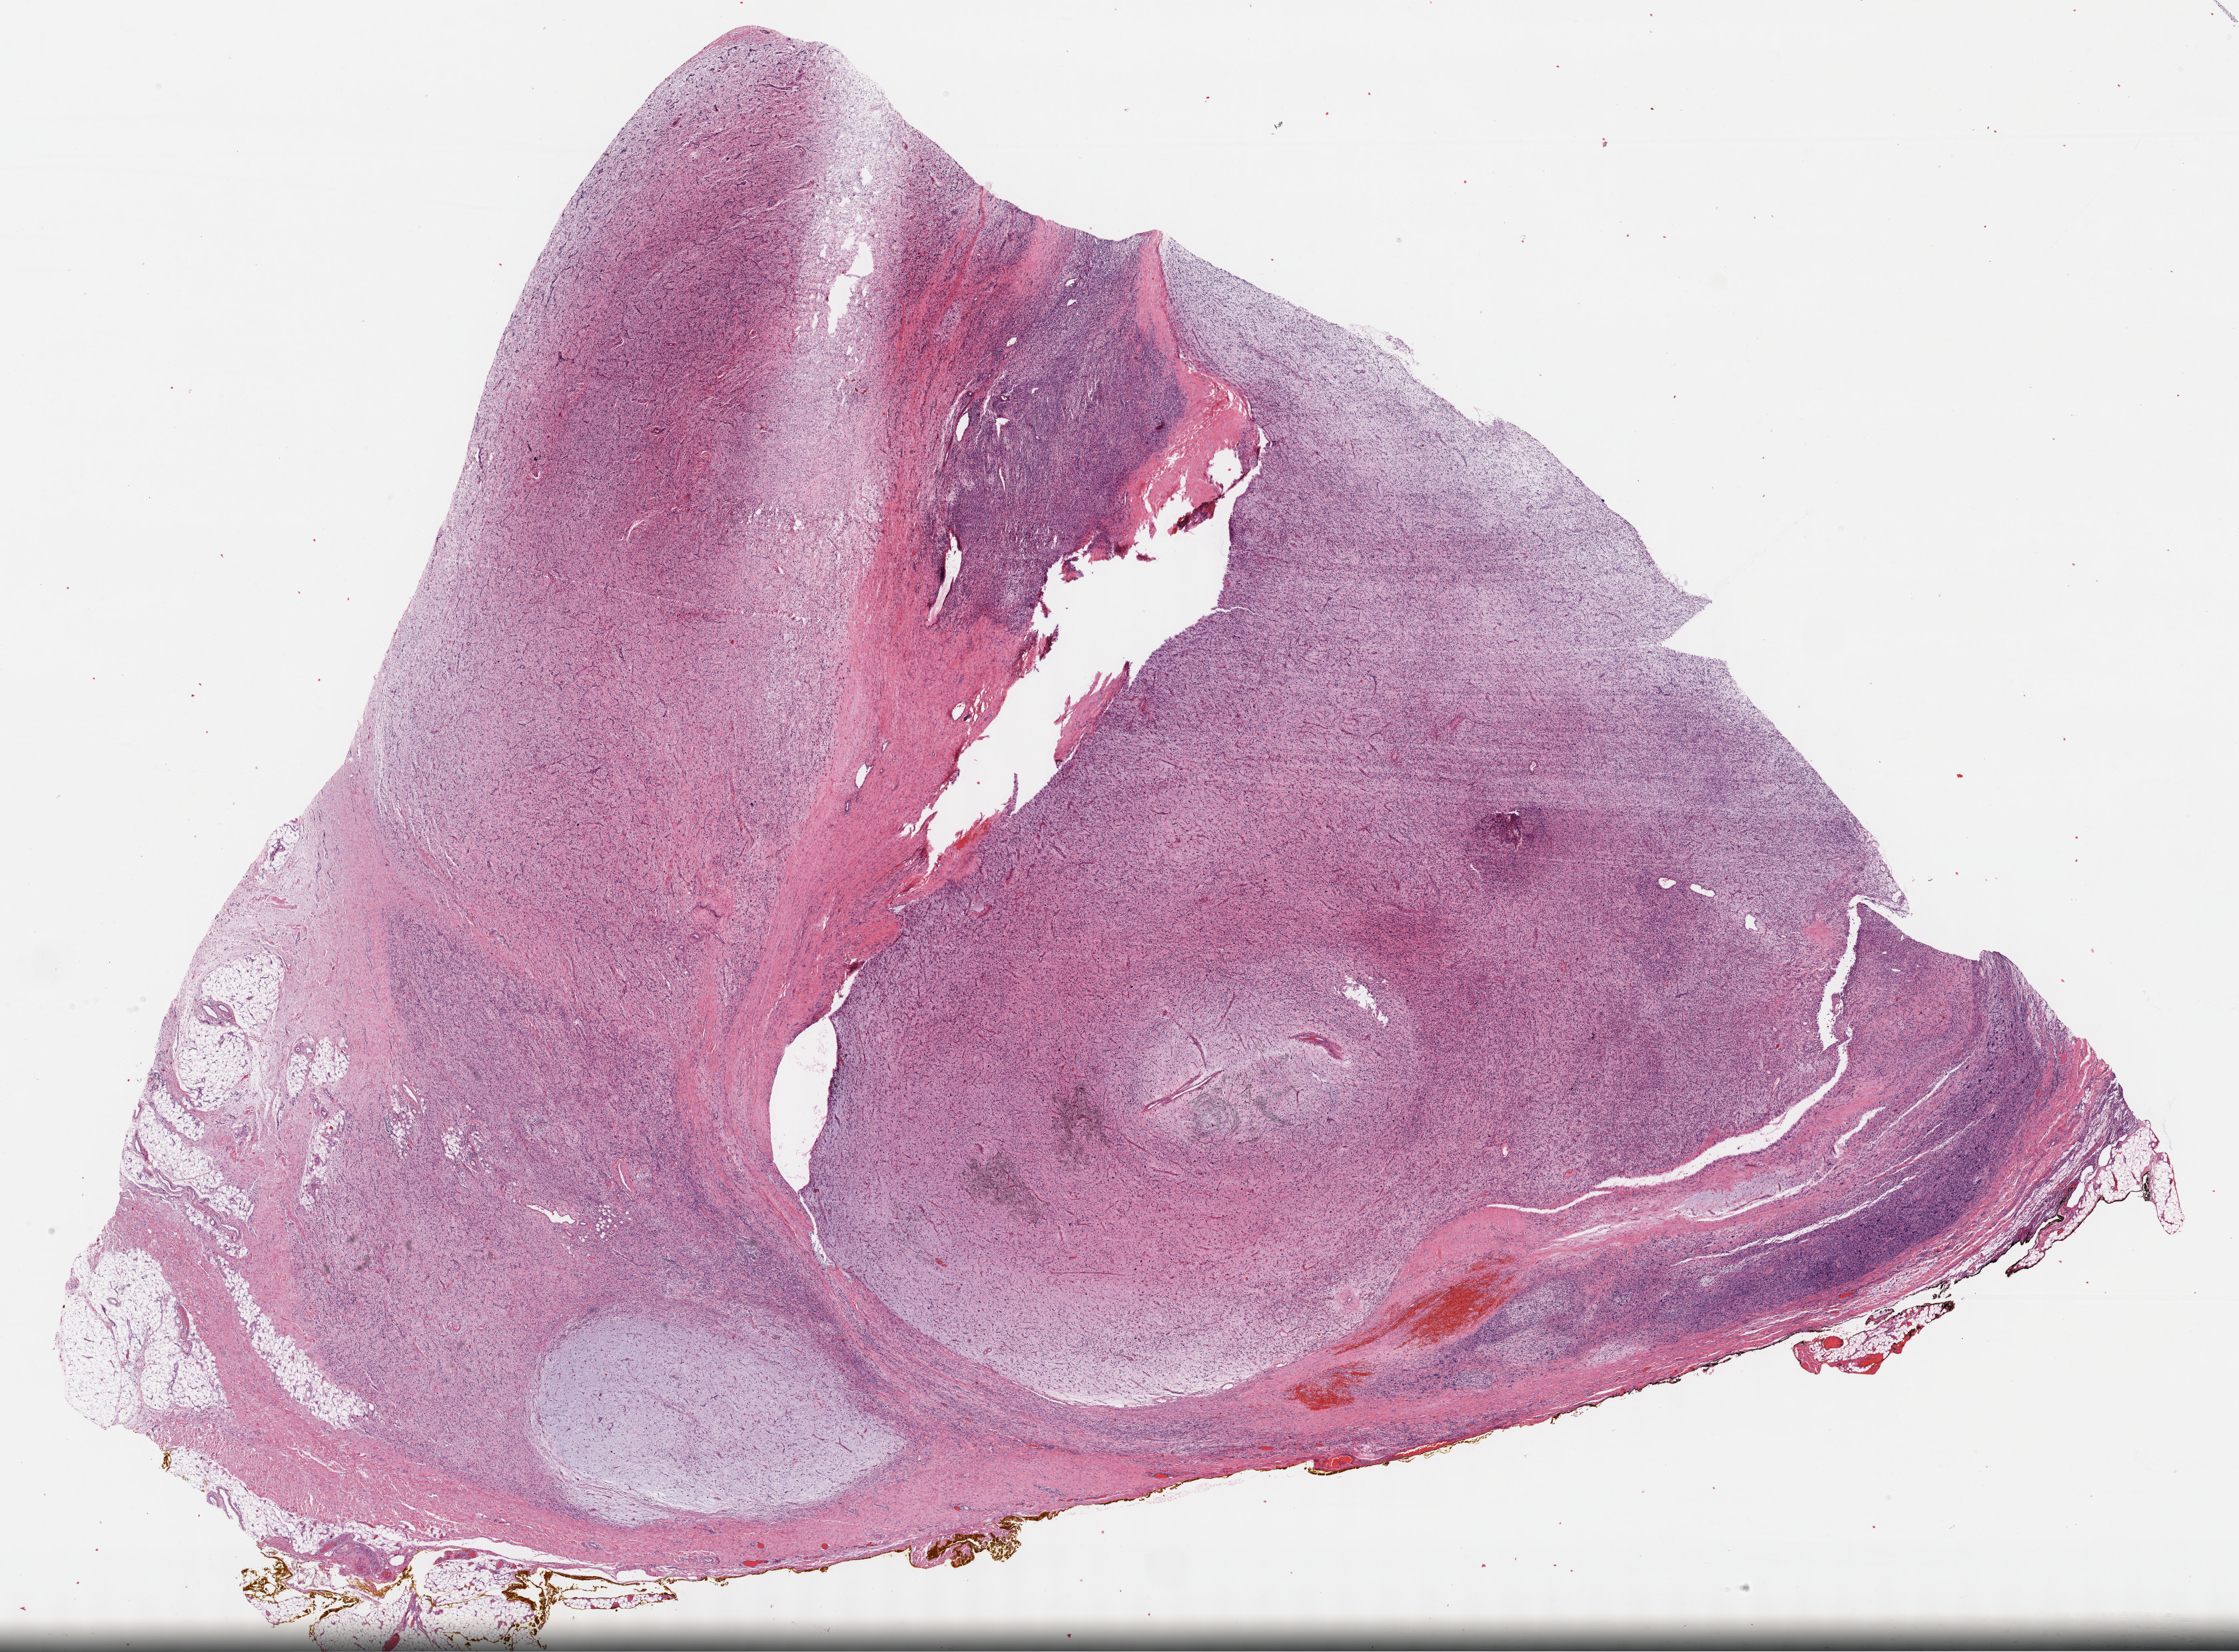
Whole-slide histology image, Hematoxylin and eosin (H&E) stained — whole scanned area (about 27.2 x 20.1 mm, from a 40x scan) shown as a low-resolution overview; FFPE section; sample: primary tumour, connective, subcutaneous and other soft tissues. Male, age 35 years at initial diagnosis.
Pathologic diagnosis: Fibromyxosarcoma (connective, subcutaneous and other soft tissues of lower limb and hip).